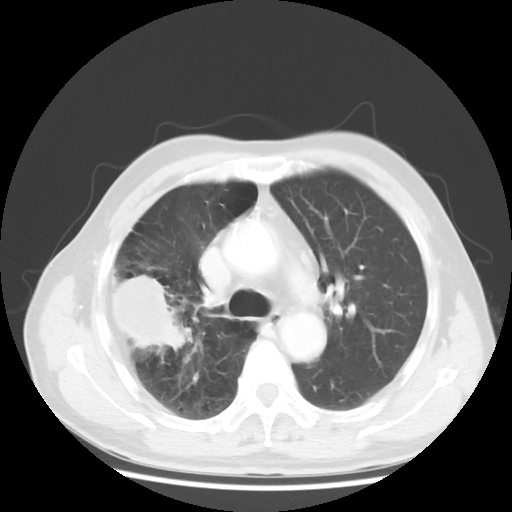
Chest CT, one axial slice. 120 kVp. Lung window (W 1500 / L -600 HU). 5 mm slice thickness. 512 × 512 image matrix, field of view 360 × 360 mm. Patient: male, 69 years. From the clinical record (not read from this slice): clinical TNM (as recorded): T3 N0 M0; histopathological grade: G3.
Annotated regions visible in this slice (bounding box drawn by a radiologist):
- lung tumour (recorded histology: adenocarcinoma): bounding box (x1, y1, x2, y2) in pixels: (110, 272, 194, 352)